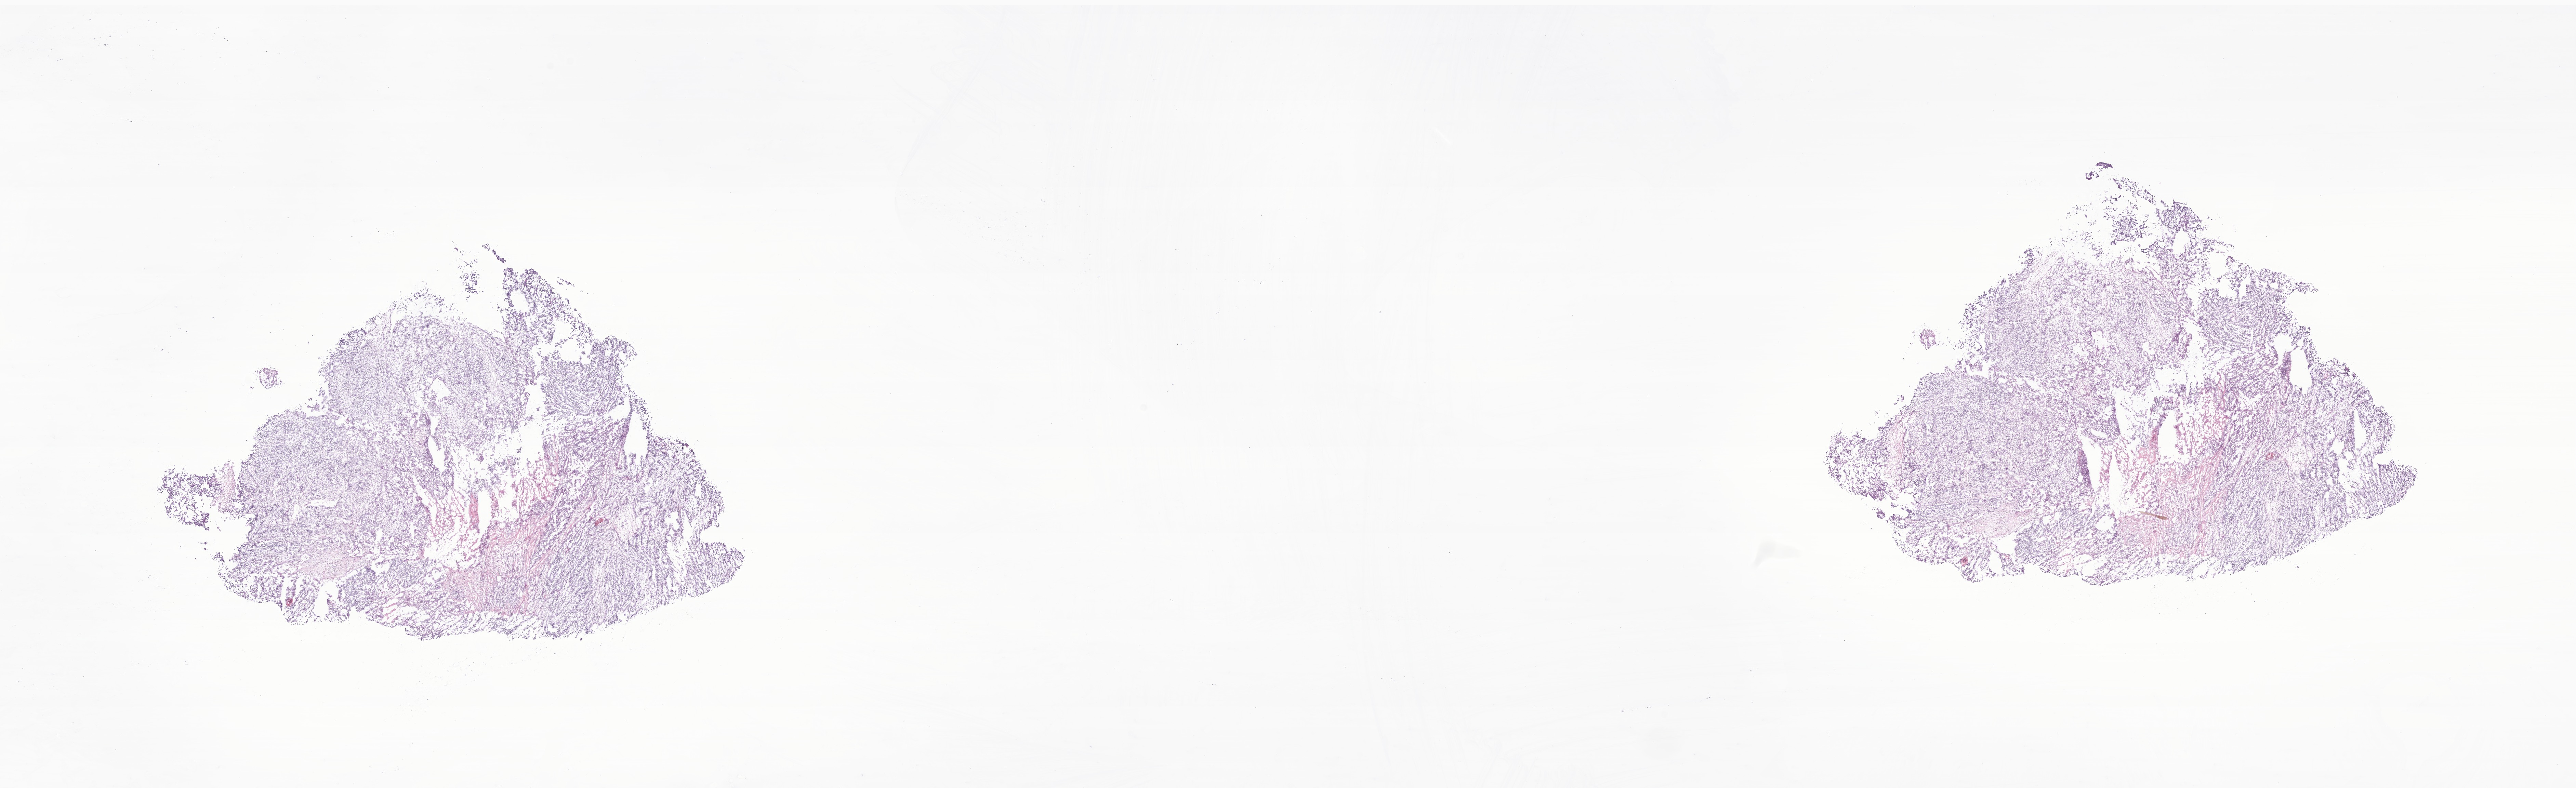
Digitized hematoxylin and eosin (H&E)-stained section of tumor tissue from the cerebellum — shown as a low-resolution overview of the whole scanned area (about 31.8 x 9.7 mm), frozen section (OCT-embedded). Patient: male, age 156 days.
- diagnosis (ICD-O-3 morphology term): Atypical teratoid/rhabdoid tumor